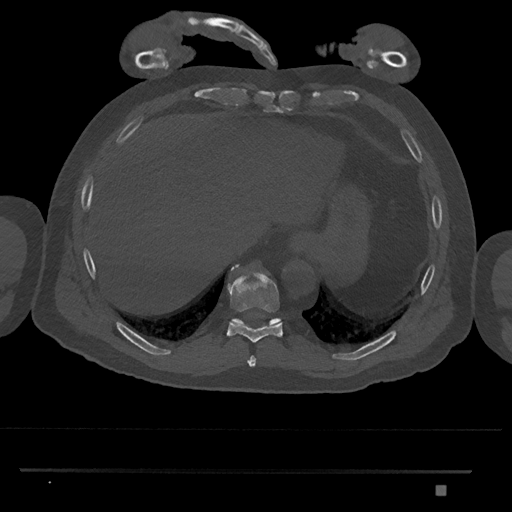
CT including the spine, one axial slice; position 1046 of 1134 along the scan axis; reconstruction kernel Br40s/3; 120 kVp; bone window (W 1800 / L 400 HU); 512 × 512 image matrix, field of view 429 × 429 mm. Patient: male, 65 years. Case-level facts recorded for this patient, not image findings: primary cancer: prostate.
Annotated regions visible in this slice (semi-automatically segmented with operator editing):
- T10 vertebra: bounding box [x1, y1, x2, y2] px = [232, 318, 281, 325]
- T8 vertebra: [247, 356, 256, 366]
- T9 vertebra: [227, 265, 283, 343]